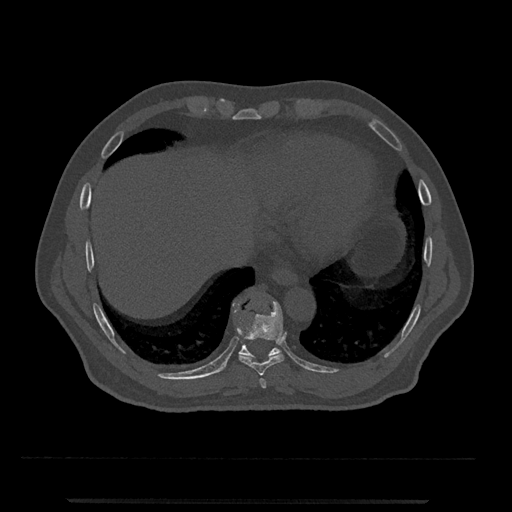
CT including the spine, one axial slice. 120 kVp. Bone window (W 1800 / L 400 HU). 512 × 512 image matrix, field of view 419 × 419 mm. Patient: male, 63 years. From the clinical record (not read from this slice): primary cancer: prostate.
Outlined on this slice (semi-automatic segmentation, software-assisted and operator-edited):
- T10 vertebra: bounding box <233,302,282,358> (left, top, right, bottom; pixels)
- T8 vertebra: <259,378,267,388>
- T9 vertebra: <237,302,285,376>